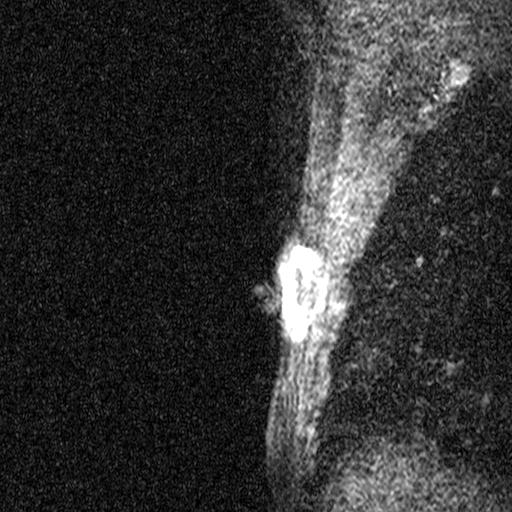
Breast MRI (dynamic contrast-enhanced), one sagittal slice; position 33 of 44 along the scan axis; dynamic contrast-enhanced study with each time point stored as its own series, time point 2 of 3 at this slice position (early post-contrast, ordered by acquisition time); 1.5 T; TE 4.5 ms, TR 11 ms; 512 × 512 image matrix, field of view 200 × 200 mm. Patient: female, 45 years. Case-level facts recorded for this patient, not image findings: setting: breast cancer imaged before/during neoadjuvant chemotherapy; receptor status: HR-positive, HER2-negative.
Annotated regions visible in this slice (semi-automatic segmentation, software-assisted and operator-edited):
- analysis volume of interest (the breast-tissue region the enhancement analysis was run in; not a lesion): bounding box <256,218,328,359> (left, top, right, bottom; pixels)
- tumour enhancement mask (voxels above the 90 % enhancement threshold inside the analysis volume of interest): <286,249,322,310>